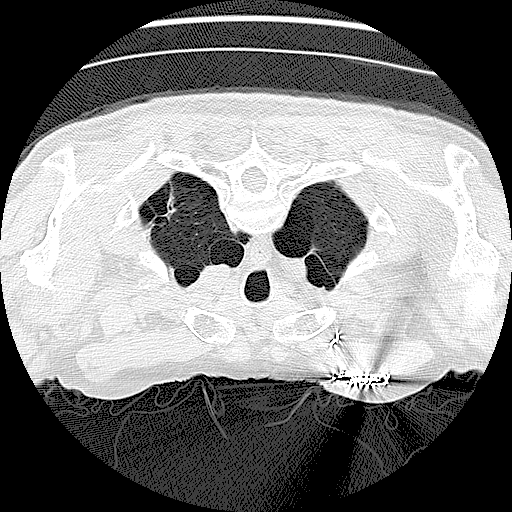
Low-dose screening chest CT, one axial slice; slice 122 of 138 in the series (ordered by position); 120 kVp; lung window (W 1500 / L -600 HU); 2.5 mm slice thickness; 512 × 512 image matrix.
Structures marked on this image (manually delineated by an expert):
- lesion 1 (tumor): box from (x=160, y=188) to (x=177, y=224) px